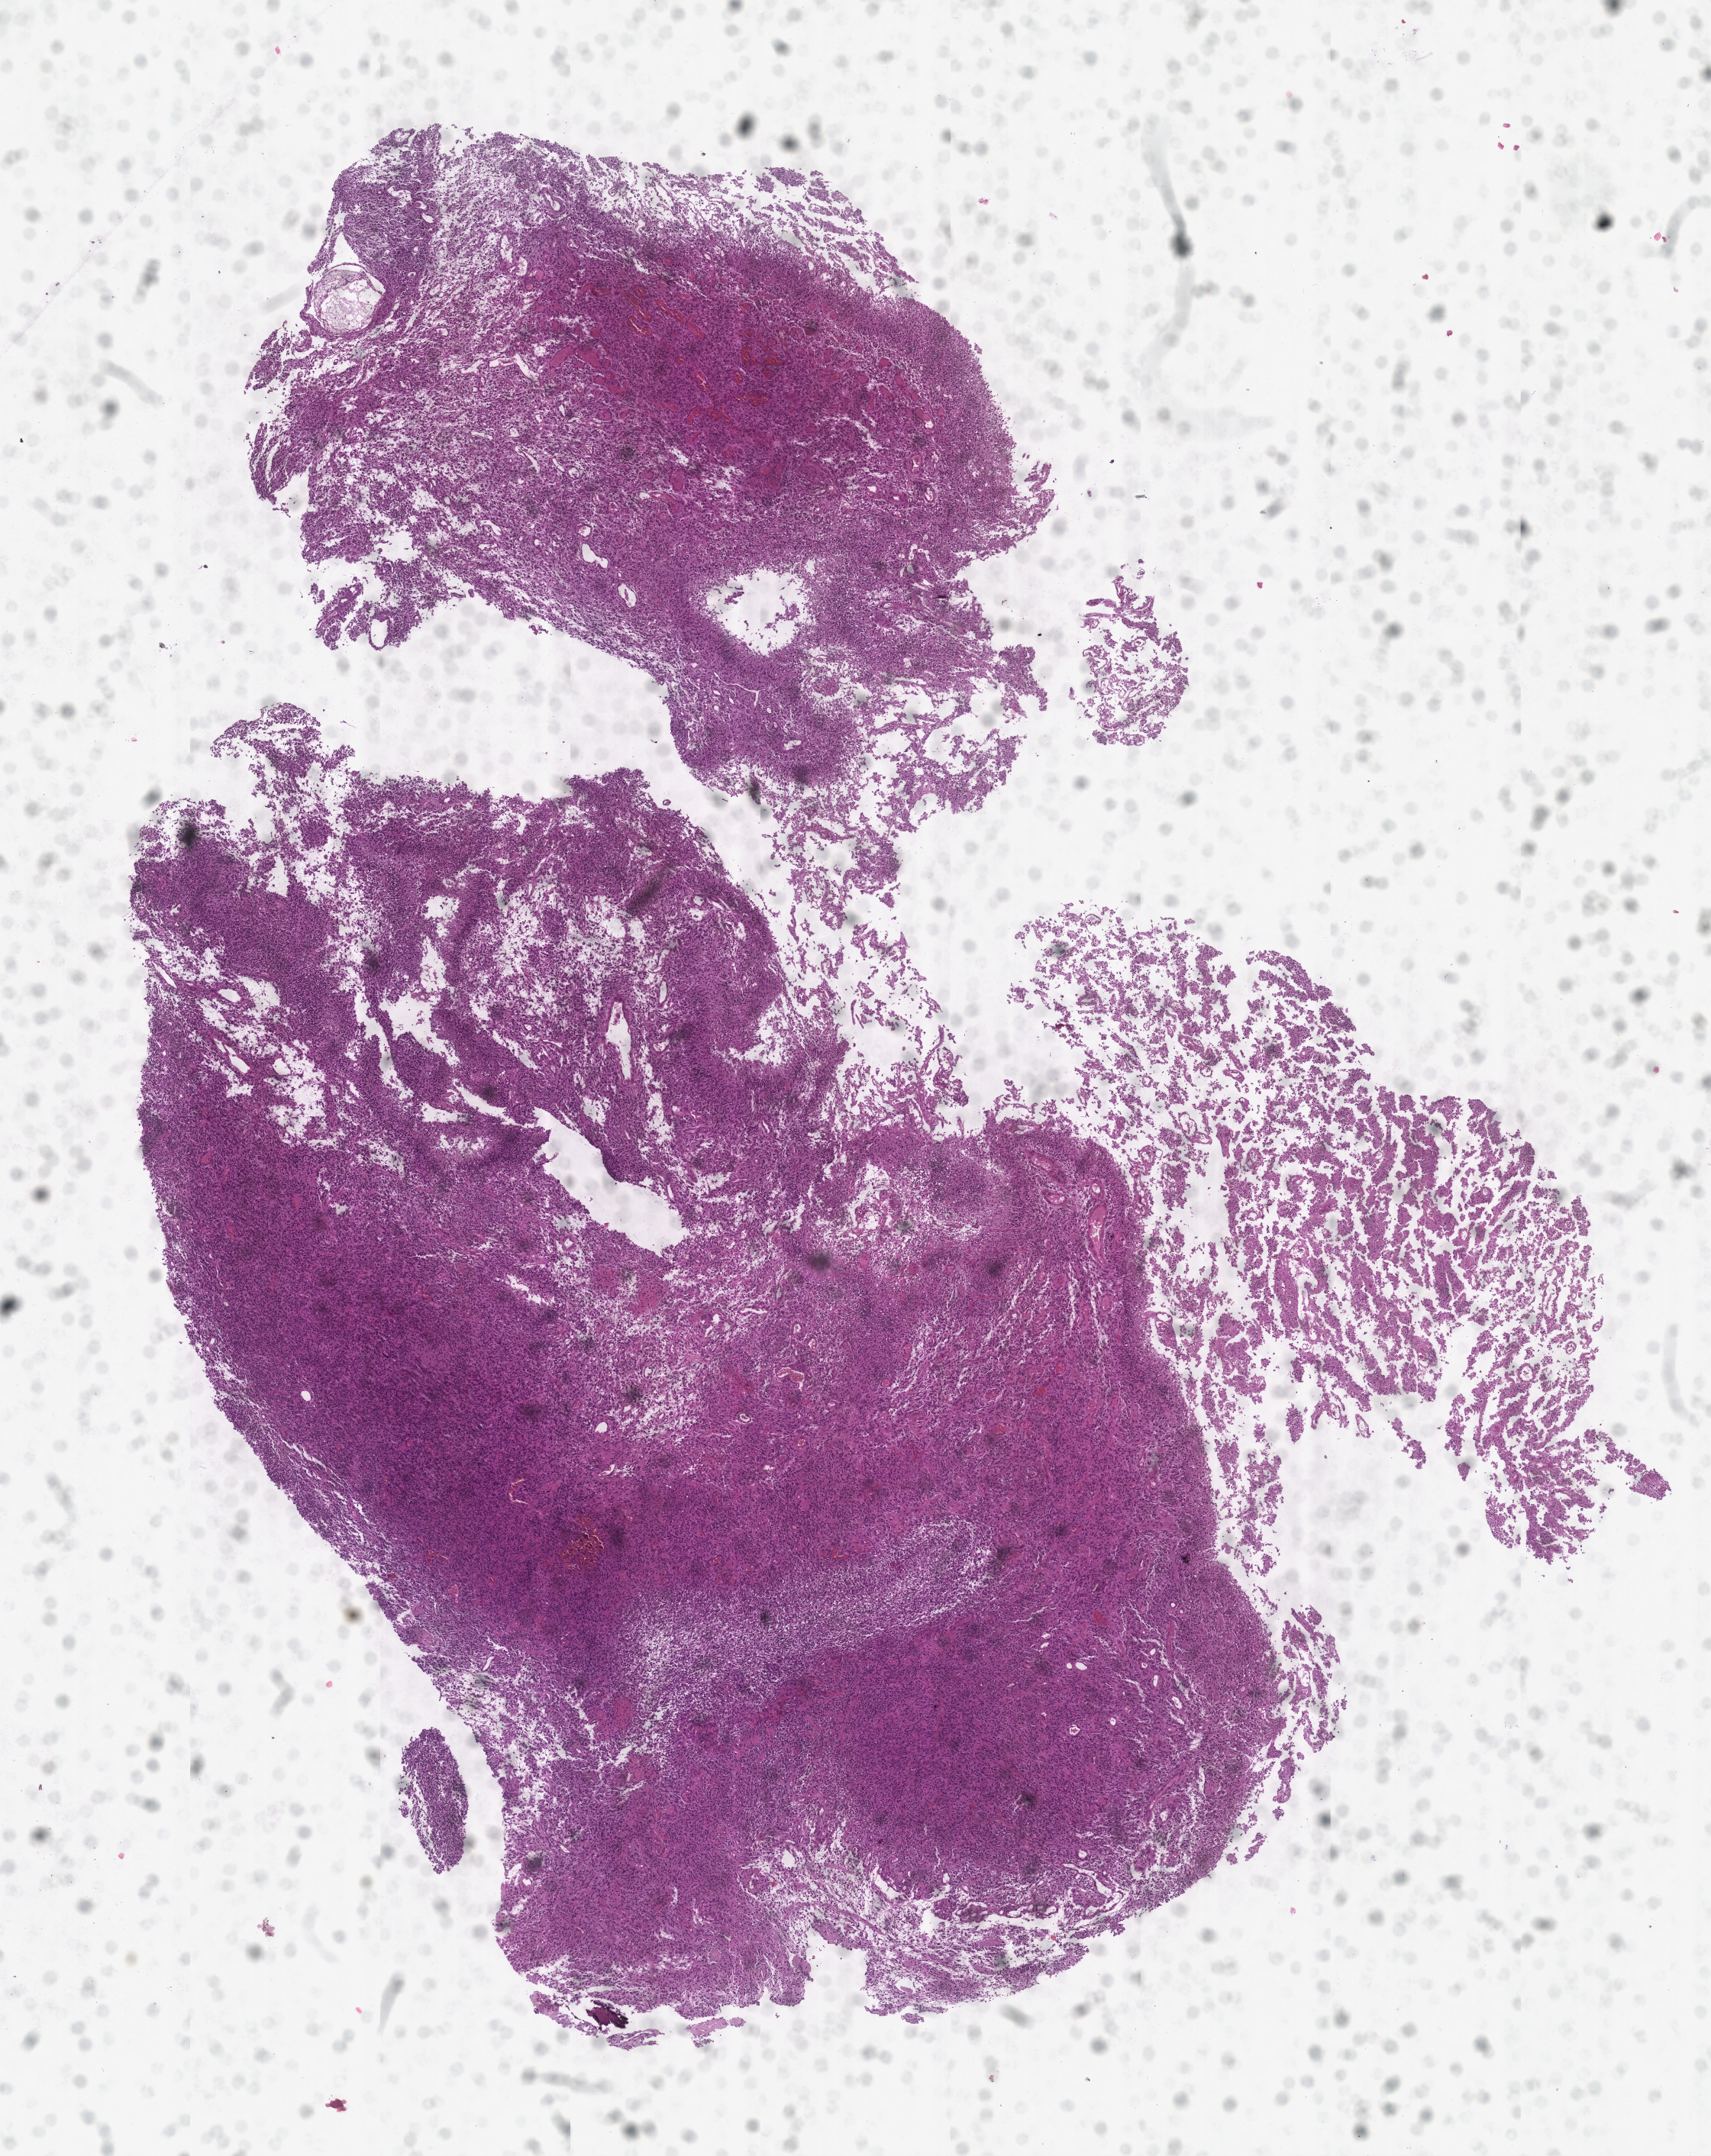
Digitized H&E-stained tissue section (whole slide) — whole scanned area (about 9.0 x 11.4 mm) shown as a low-resolution overview. Brain, tumour tissue. 71-year-old male patient.
Histologic diagnosis: Glioblastoma.